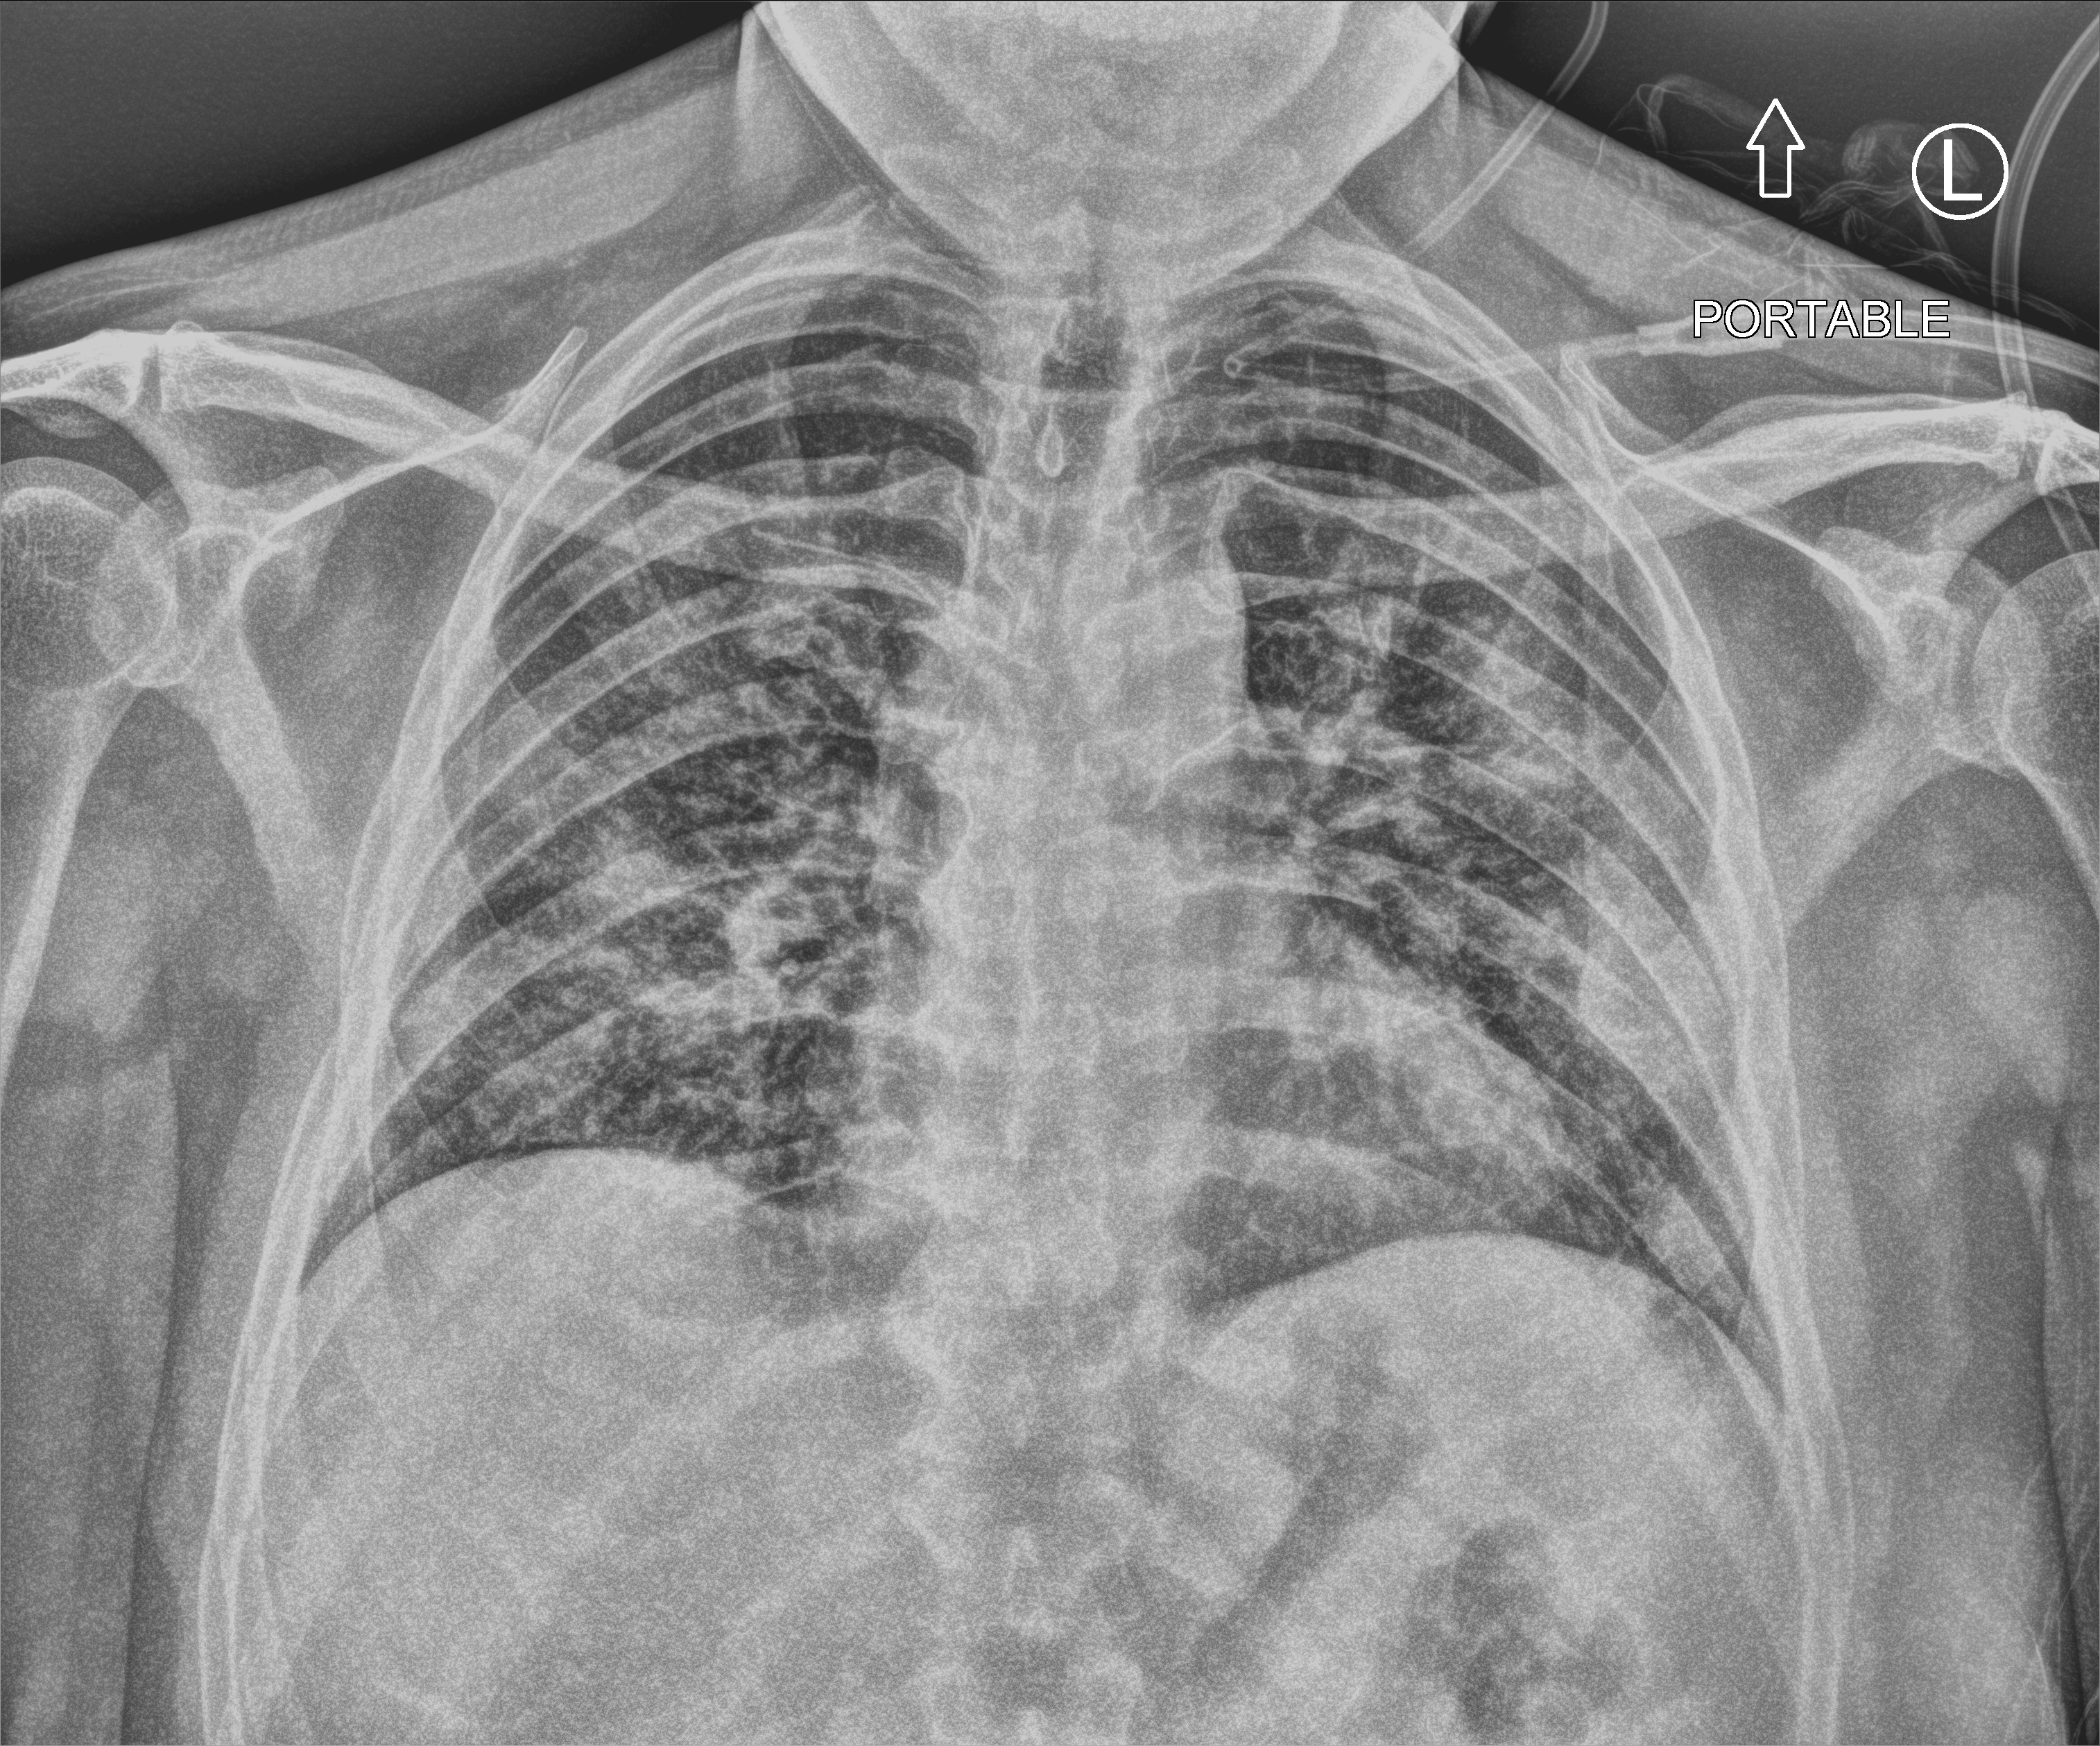
Portable chest radiograph; anteroposterior (AP) projection. Patient hospitalised with COVID-19; male, aged 18–59 years.
Admission-level facts for this patient (not findings on this image; timing relative to this image not recorded): diabetes (admission record): yes; admitted to intensive care during this hospital stay: no; mechanically ventilated during this hospital stay: no.